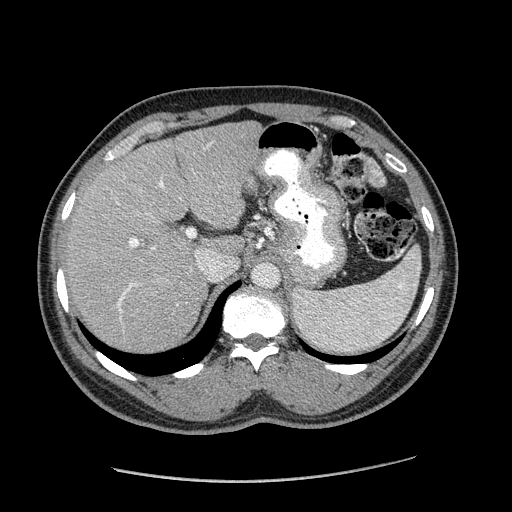
Contrast-enhanced abdominal CT (liver protocol), one axial slice; position 127 of 182 along the scan axis; reconstruction kernel STANDARD; 120 kVp; soft-tissue window (W 400 / L 40 HU); 512 × 512 image matrix. From the clinical record (not read from this slice): diagnosis: hepatocellular carcinoma (patient treated with transarterial chemoembolisation; whether this scan precedes or follows treatment is not stated here); TNM stage (as recorded): Stage-I; Child-Pugh class: A; tumour differentiation: well differentiated; tumour size: 3.1 cm.
Annotated regions visible in this slice (semi-automatically segmented with operator editing):
- liver parenchyma outside the tumour (the mass and vessels are separate outlines, so this box may not span the whole liver): box from (x=65, y=120) to (x=262, y=350) px
- liver vessels: (x=116, y=181)–(x=165, y=312)